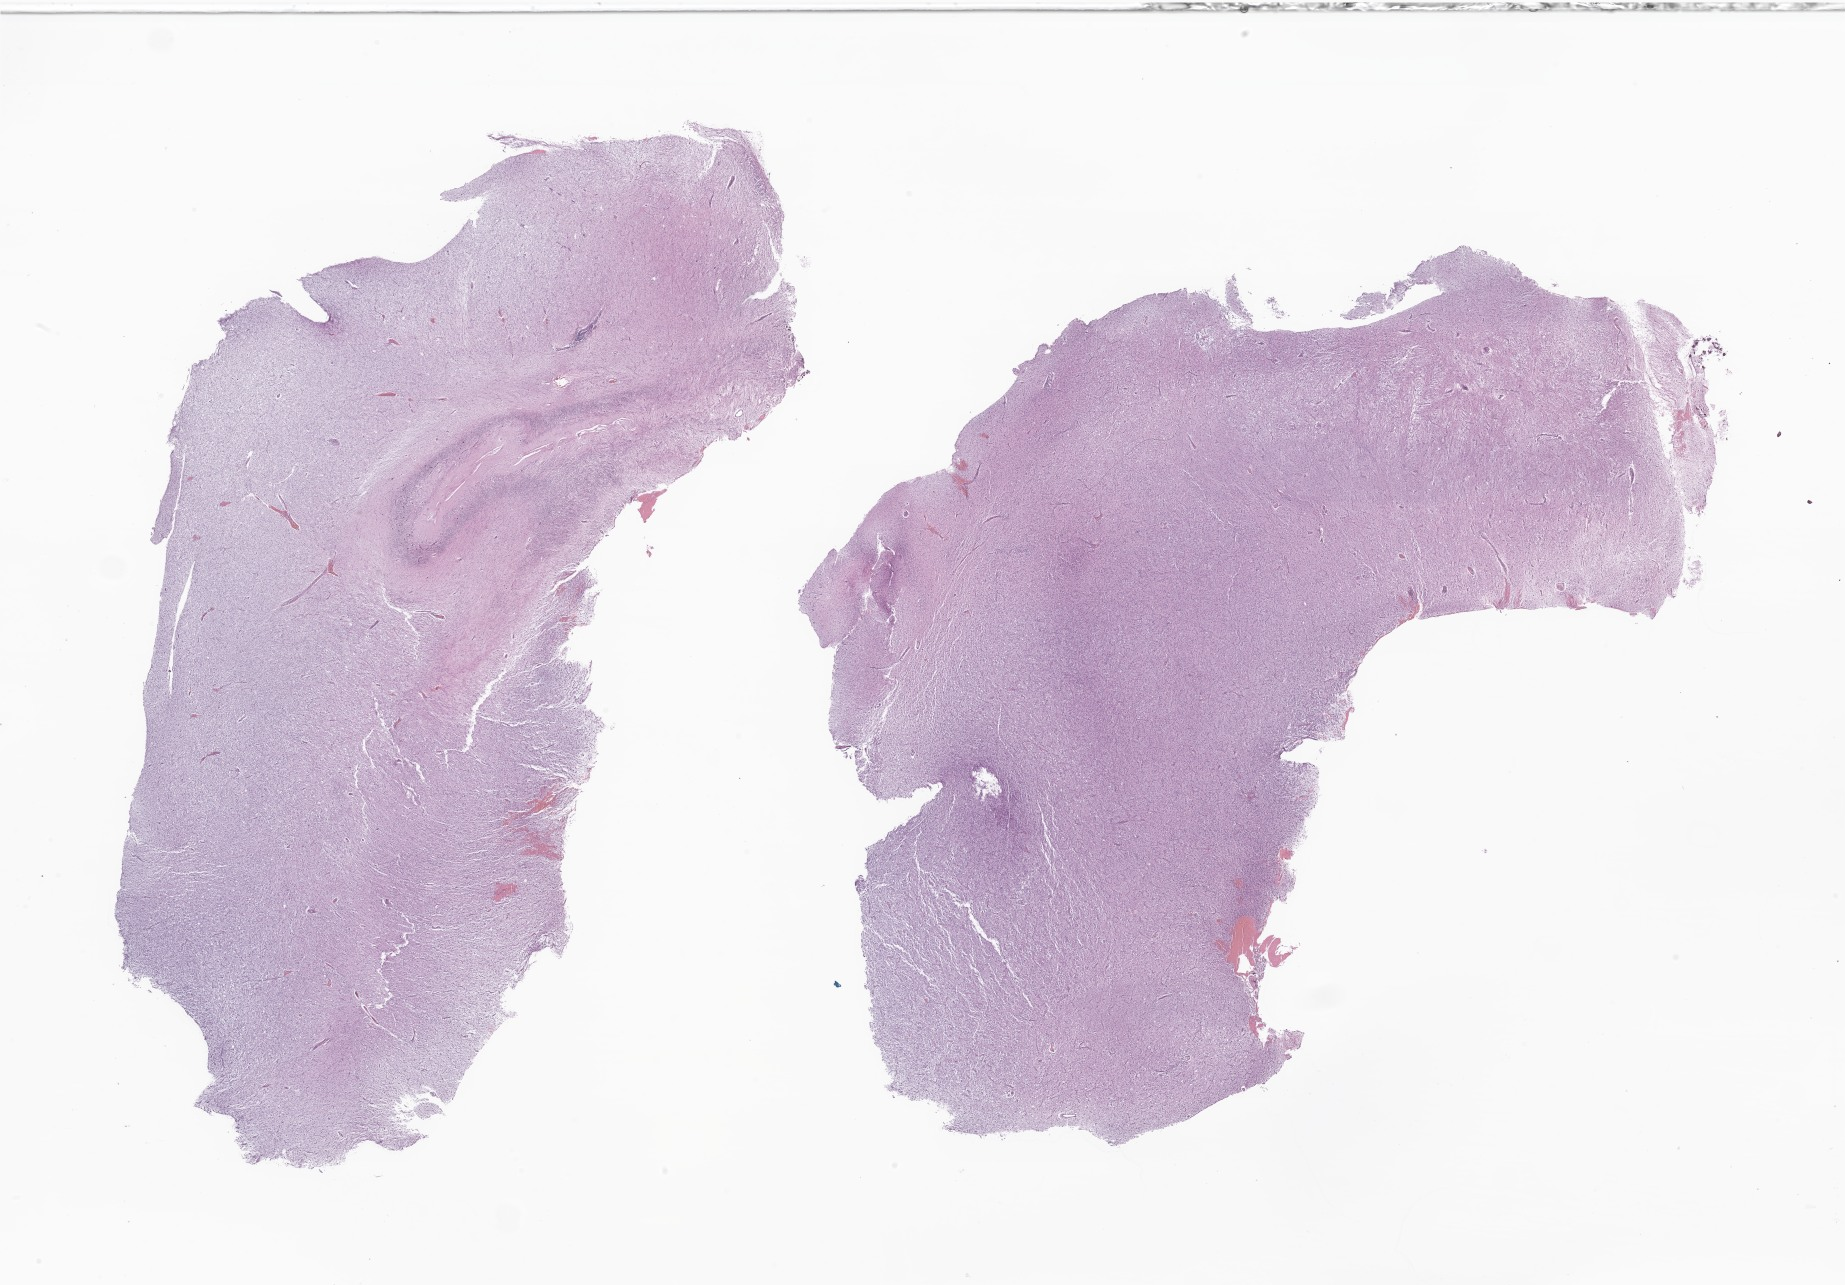
Whole-slide image, haematoxylin and eosin stain of tumor tissue from the cerebral ventricle — a low-resolution overview of the entire scanned area, about 31.1 x 21.7 mm. Formalin-fixed, paraffin-embedded (FFPE) tissue. Patient: female, age 131 months (10 years 11 months).
Recorded diagnosis: Tumor cells, uncertain whether benign or malignant.